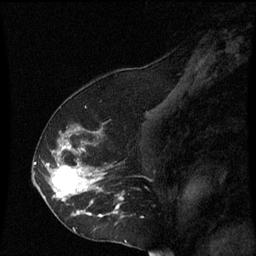
Breast MRI (dynamic contrast-enhanced), one sagittal slice. Position 38 of 60 along the scan axis. Dynamic contrast-enhanced series, image 2 of 3 at this slice position (ordered by acquisition). 1.5 T. TE 4.2 ms, TR 8.9 ms. 2 mm slice thickness. 256 × 256 image matrix, field of view 200 × 200 mm. Patient: female, 53 years. From the clinical record (not read from this slice): setting: breast cancer imaged before/during neoadjuvant chemotherapy; receptor status: HR-positive, HER2-negative.
Outlined on this slice (semi-automatically segmented with operator editing):
- analysis volume of interest (the breast-tissue region the enhancement analysis was run in; not a lesion): box from (x=38, y=128) to (x=125, y=231) px
- tumour enhancement mask (voxels above the 70 % enhancement threshold inside the analysis volume of interest): (x=46, y=140)–(x=121, y=217)